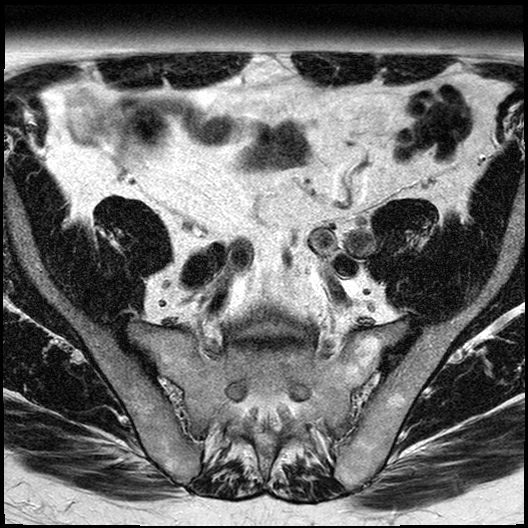
Prostate MRI examination; 3 images, each a single mid-volume slice chosen by position (not for content). Treatment context recorded for this patient: No surgery.
Image 1: axial T2-weighted image, series "T2W_TSE_AX5MM", slice 19 of 36, 5 mm slice thickness.
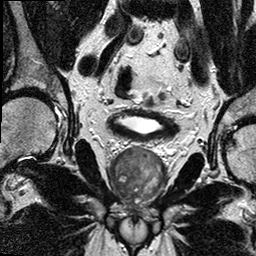
Image 2: T2-weighted coronal slice, series "T2W_TSE_COR", slice 15 of 28, 3 mm slice thickness.
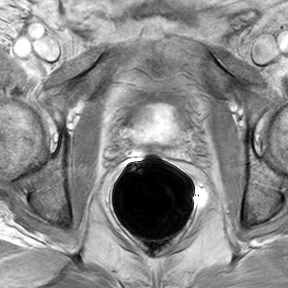
Image 3: axial dynamic contrast-enhanced (DCE) T1-weighted image, series "AX BLISS_GAD_8", slice 17 of 32, dynamic phase 5 of 8, 6 mm slice thickness.
MRI report (verbatim):
The prostate has a maximal lateral diameter of 4.4 cm, a maximal craniocaudal diameter of 4.2 cm and a maximal AP diameter of 3.0 cm resulting in an estimated gland volume of 29 cc. The zonal anatomy is preserved. In the left posterior lateral peripheral zone, mid third of the prostate, between 4 and 5:00 there is a geographic 9 x 7 mm T2-hypointense area seen, which shows suspicious wash-in and washout kinetics on the dynamic series. (slice location 24, image 67, series 1205; precise location 39 image 14 series 401; please note that the slice location is not consistent since the patient was repositioned during the exam). The adjacent neurovascular bundle is not involved. No evidence of extracapsular extension. There is the same level (image 67 series 1205) there is a second 6 x 5 mm area of suspicious T2- Hypointensity and geographic configuration with suspicious enhancement seen in the anterior centrum gland anteriorly paramedian, just posterior to the fibromuscular band. No evidence for involvement of the neurovascular bundle on either side. No evidence for seminal vesicles infiltration.No evidence of involvement of bladder neck and rectal wall. No suspiciously enlarged obturator and iliac lymph nodes. IMPRESSION: 1) 7 x 9 mm tumor in the left peripheral zone, midthird of the prostate. Possible second small 6 mm focus in the paramedian right anterior central gland posterior to the fibromuscular band. 2) No evidence of extraglandular disease. Neurovascular bundles uninvolved. 3) No evidence for seminal vesicles infiltration. 4) No suspiciously enlarged obturator and iliac lymph nodes.

Pathology / management note recorded for this patient (as recorded; not read from these images):
Active surveillance – no bx or surgery as yet; dx in 7 yrs previous with gleason 6, 7 prostate cancer under active surviellence on finasteride for rising PSA. Most recent PSA in 5.91.